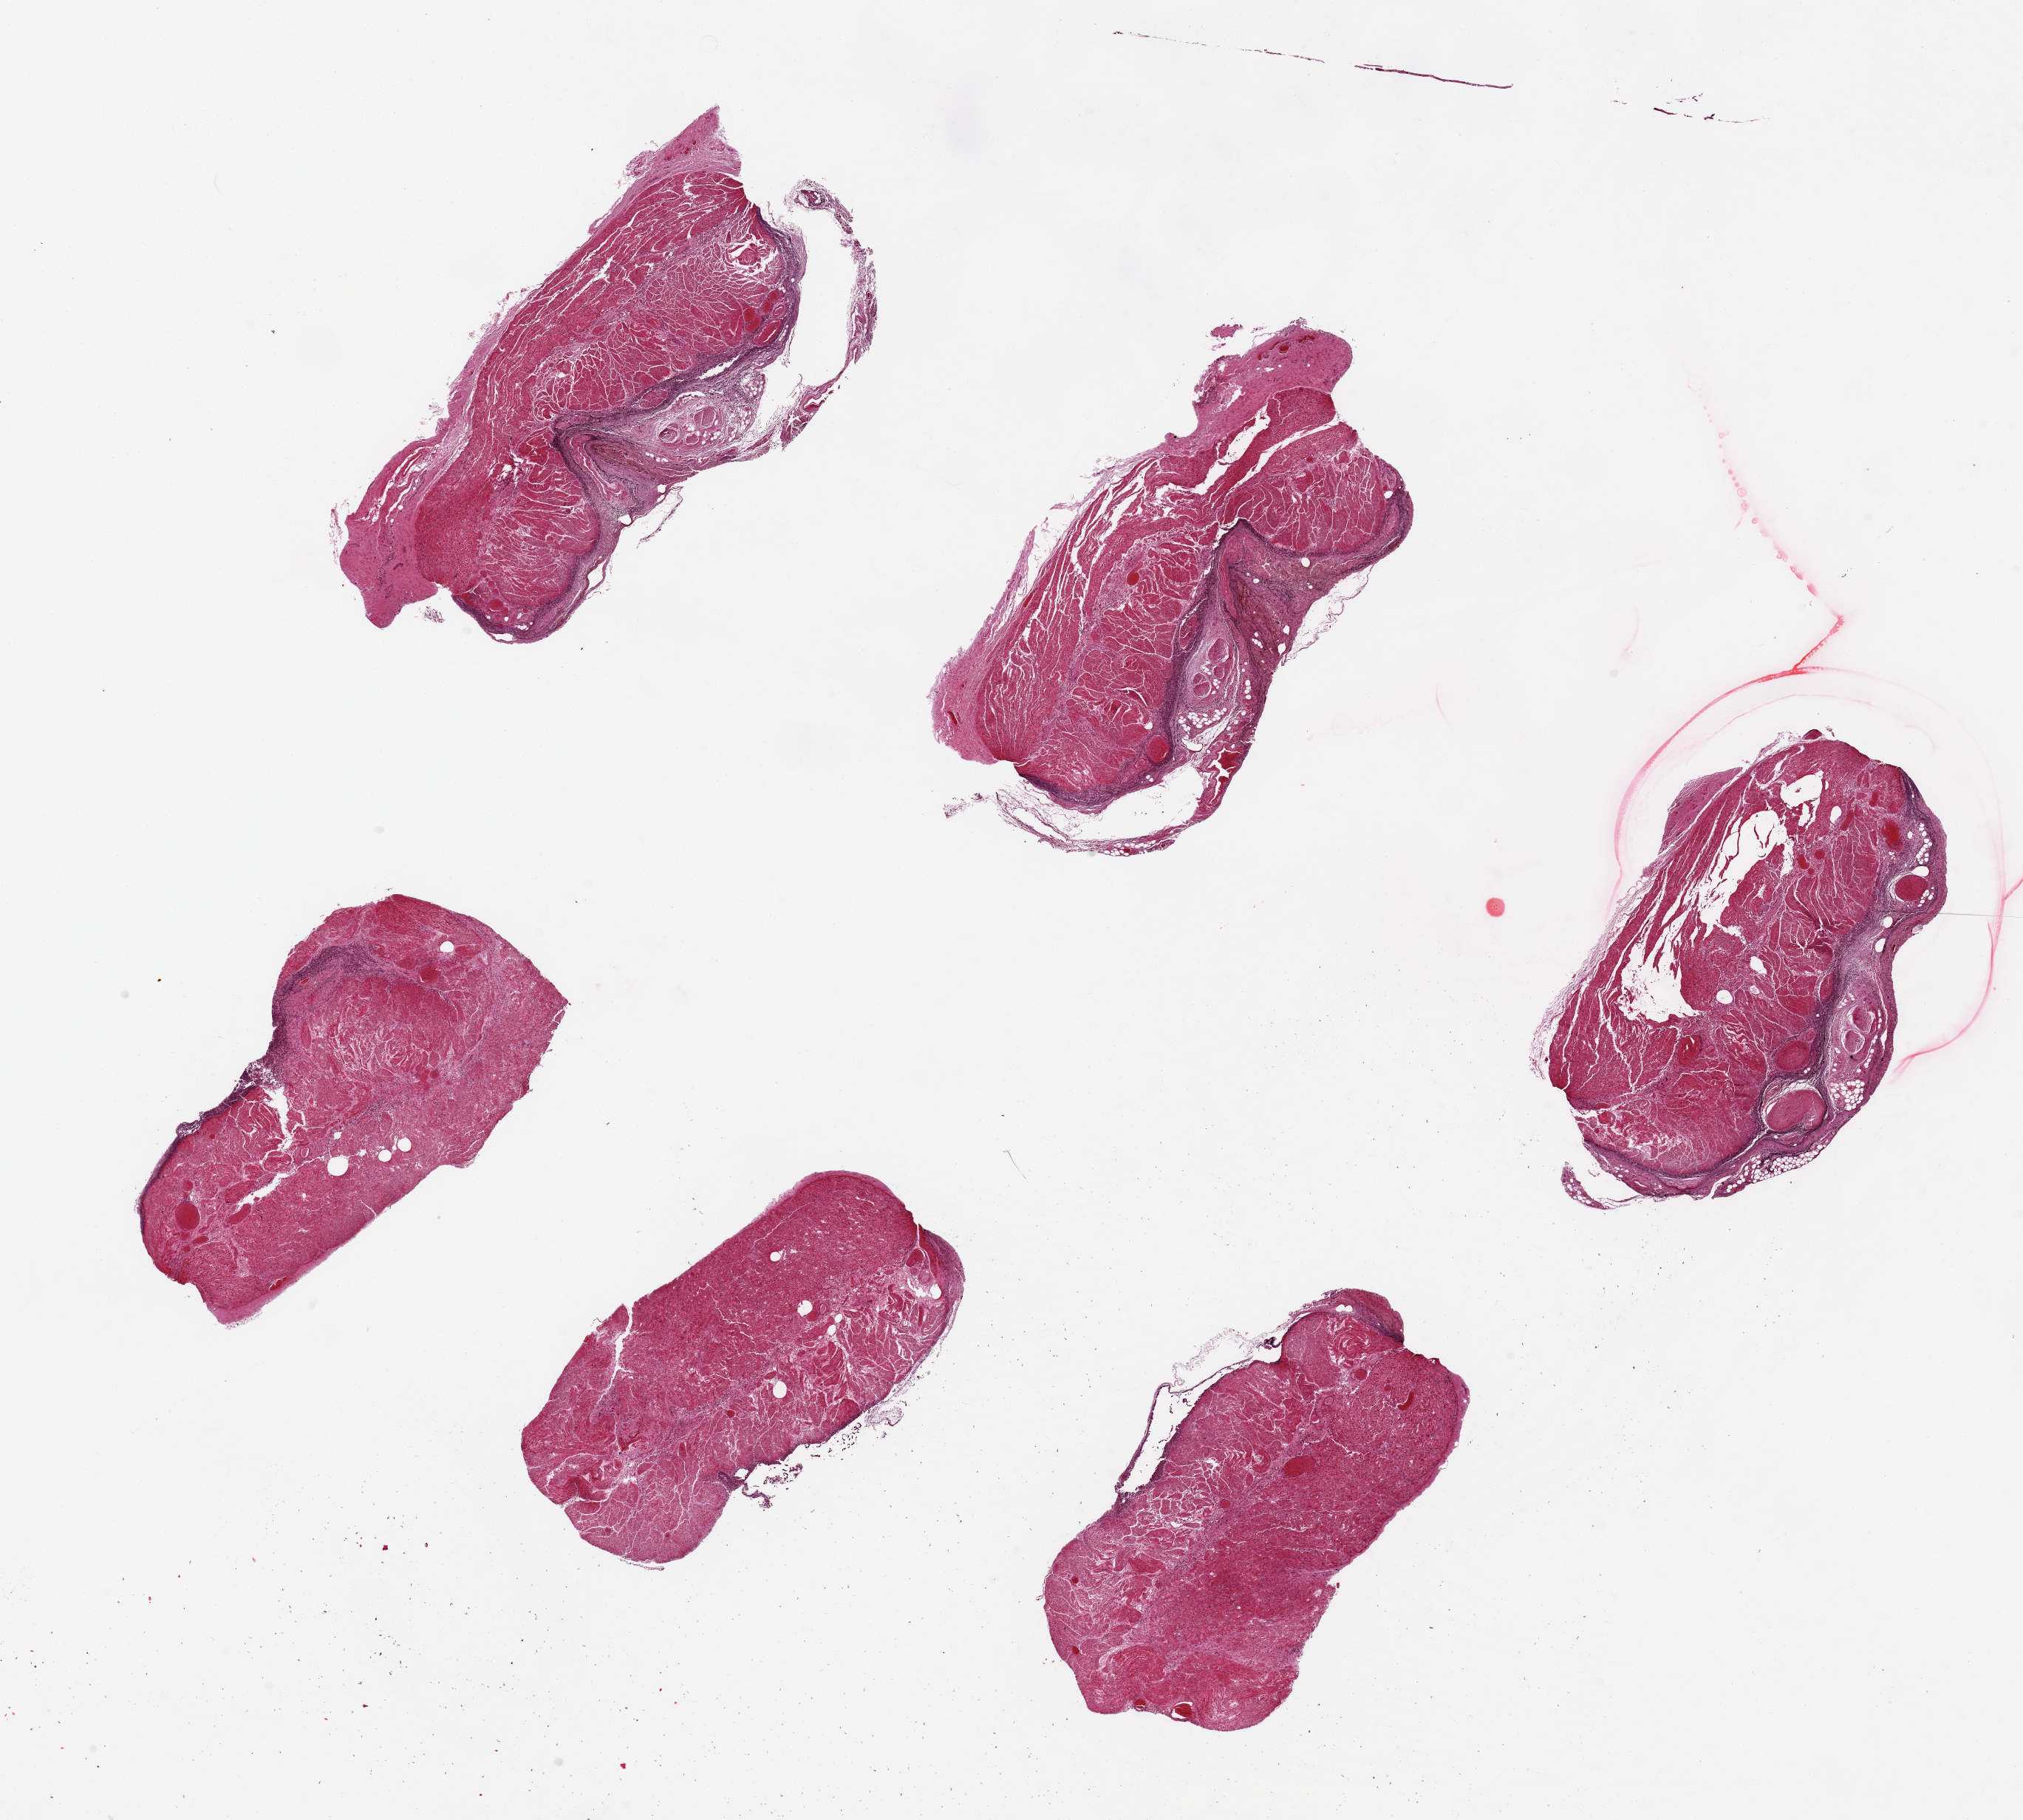
Digitized H&E-stained section, whole scanned area (about 21.7 x 19.5 mm, from a 20x scan) shown as a low-resolution overview; PAXgene-fixed paraffin-embedded (PFPE) section; section of esophageal muscle (target tissue); donor tissue sample. Donor: male.
Pathologist's review note for this sample: 6 pieces,several with badly autolyzed ? mucosa/ inflammatory debris; unusually severe autolysis makes assessment impossible.